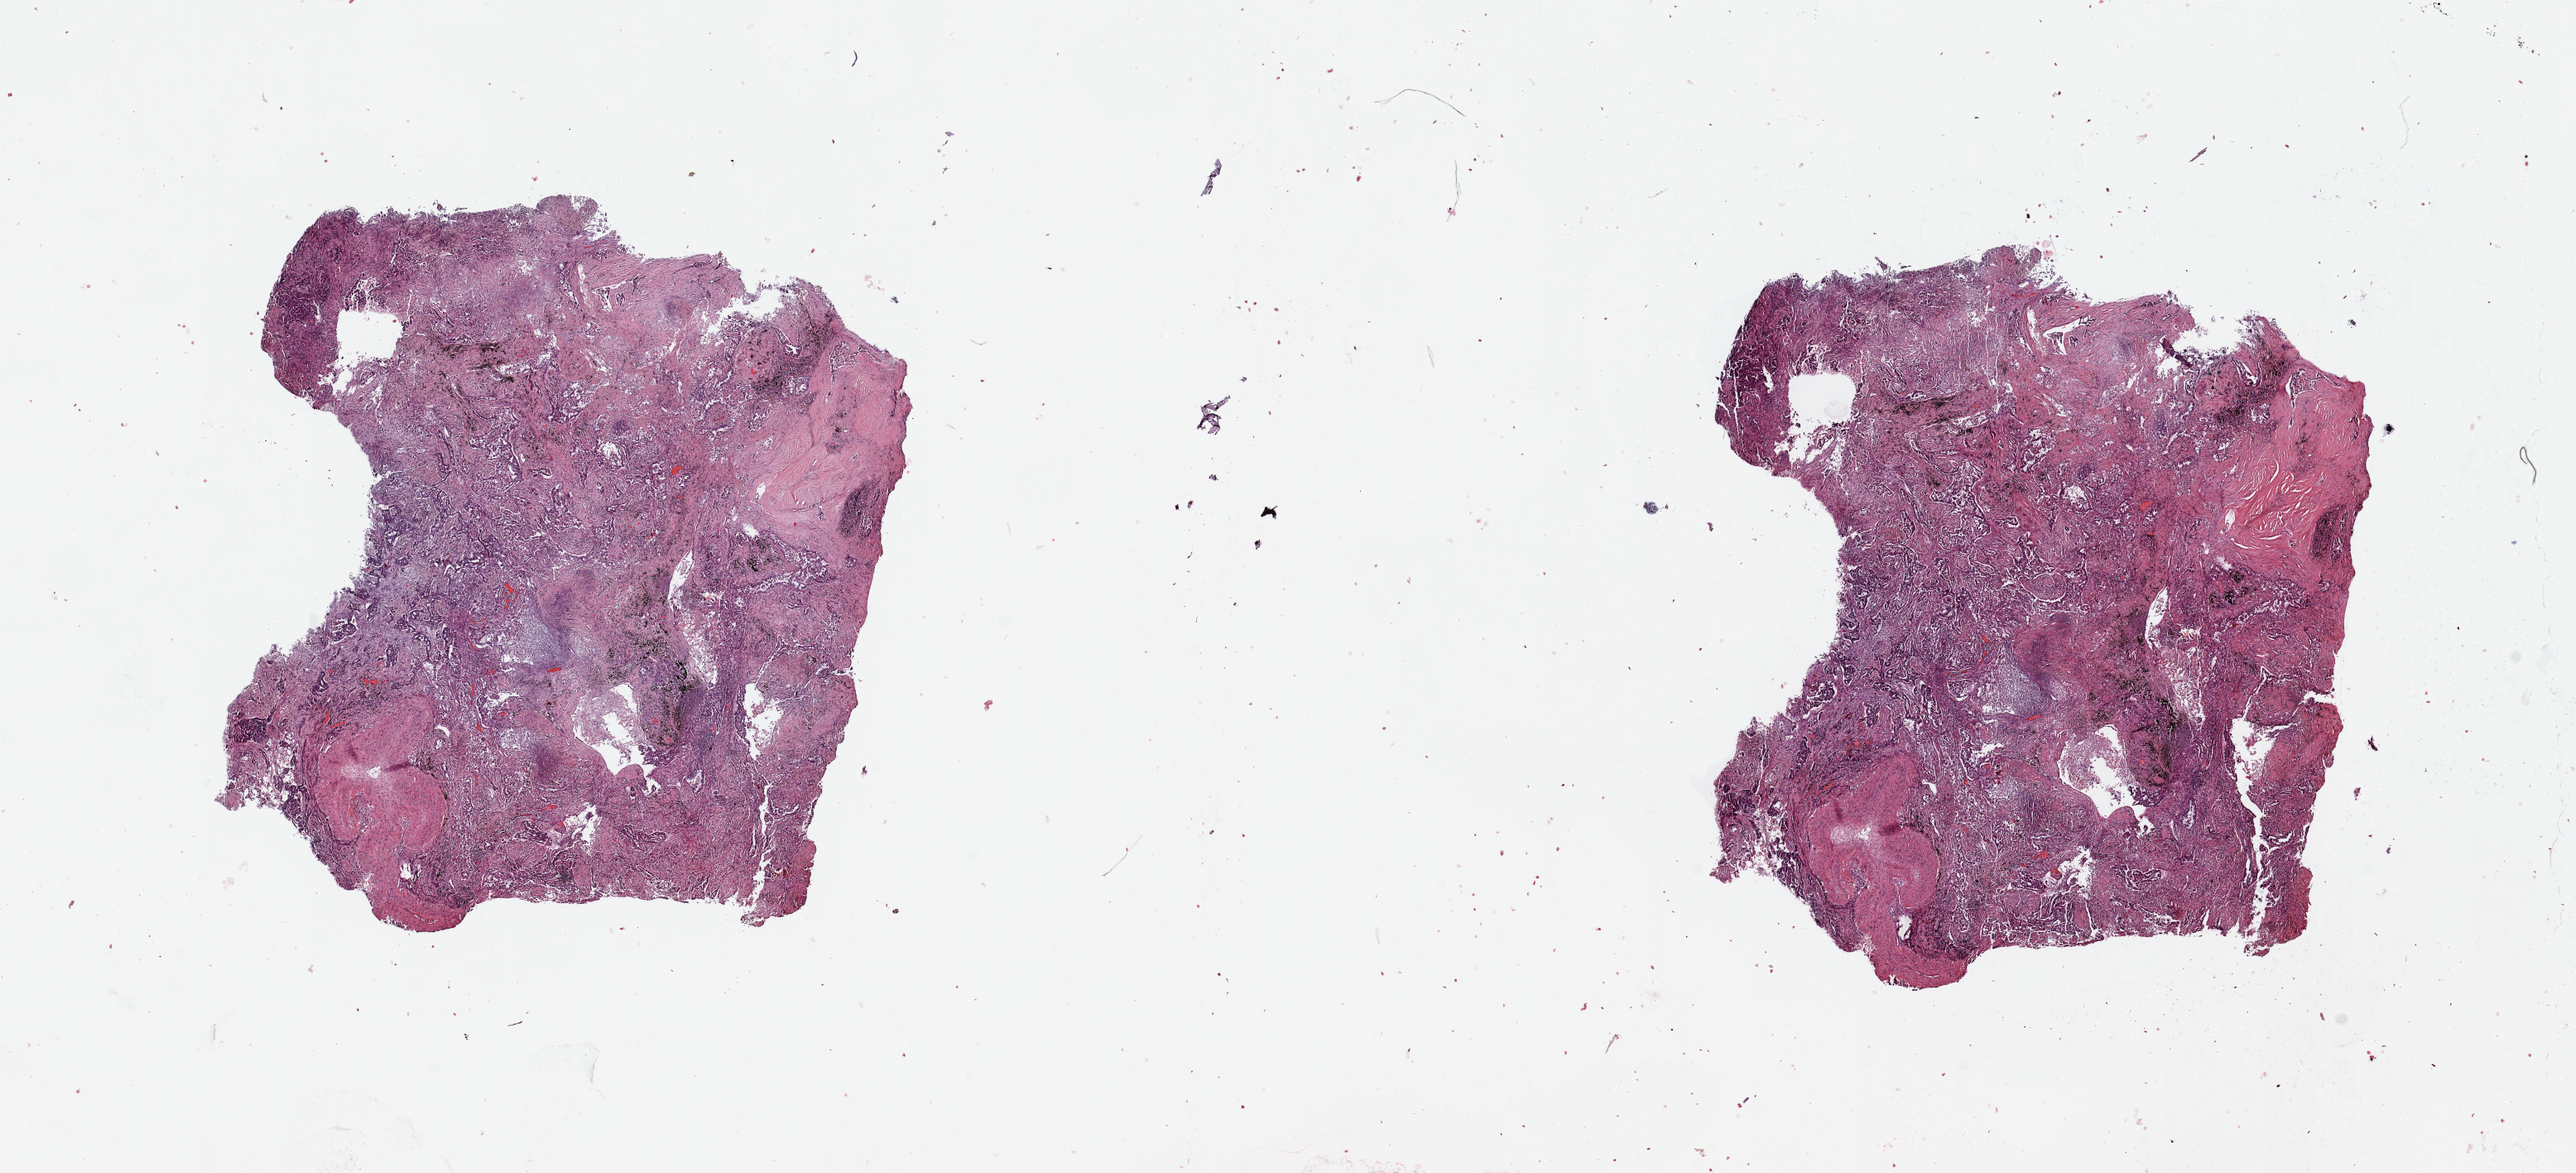
Whole-slide histology image, H&E-stained, whole scanned area (about 24.6 x 11.2 mm, acquisition: 20x scan) shown as a low-resolution overview; lung, tumour tissue. Patient: male, age 59 years. Histologic grade: G3 (poorly differentiated).
AJCC pathologic stage: IB. Diagnosis: Adenocarcinoma, NOS. Primary tumour site (as recorded): right upper lobe.